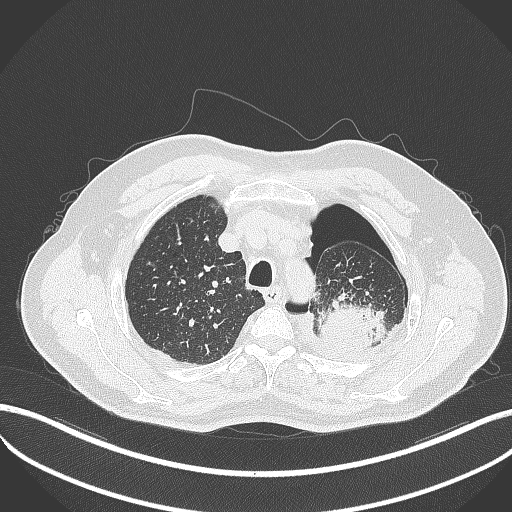
Chest CT, one axial slice. Slice 407 of 464 in the series (ordered by position). Reconstruction kernel B70f. 120 kVp. Lung window (W 1500 / L -600 HU). 512 × 512 image matrix, field of view 400 × 400 mm. Male patient, age 76 years. Case-level facts recorded for this patient, not image findings: clinical TNM (as recorded): T3 N0 M1b.
Annotated regions visible in this slice (rectangle marked by the reading radiologist):
- lung tumour (recorded histology: adenocarcinoma): bounding box [x1, y1, x2, y2] px = [313, 293, 387, 358]